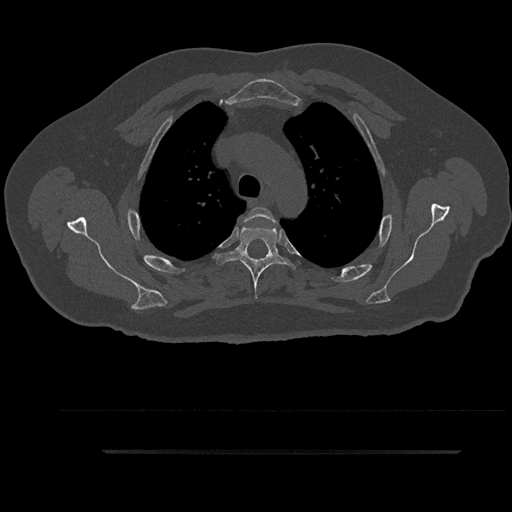
CT including the spine, one axial slice; slice 679 of 797 in the series (ordered by position); 120 kVp; bone window (W 1800 / L 400 HU); 0.5 mm slice thickness; 512 × 512 image matrix, field of view 432 × 432 mm. Male patient, age 63 years. Case-level facts recorded for this patient, not image findings: primary cancer: renal; vertebrae with lytic lesions (as recorded): T8.
Outlined on this slice (semi-automatic segmentation, software-assisted and operator-edited):
- T3 vertebra: bounding box <244,207,275,259> (left, top, right, bottom; pixels)
- T4 vertebra: <216,226,296,299>